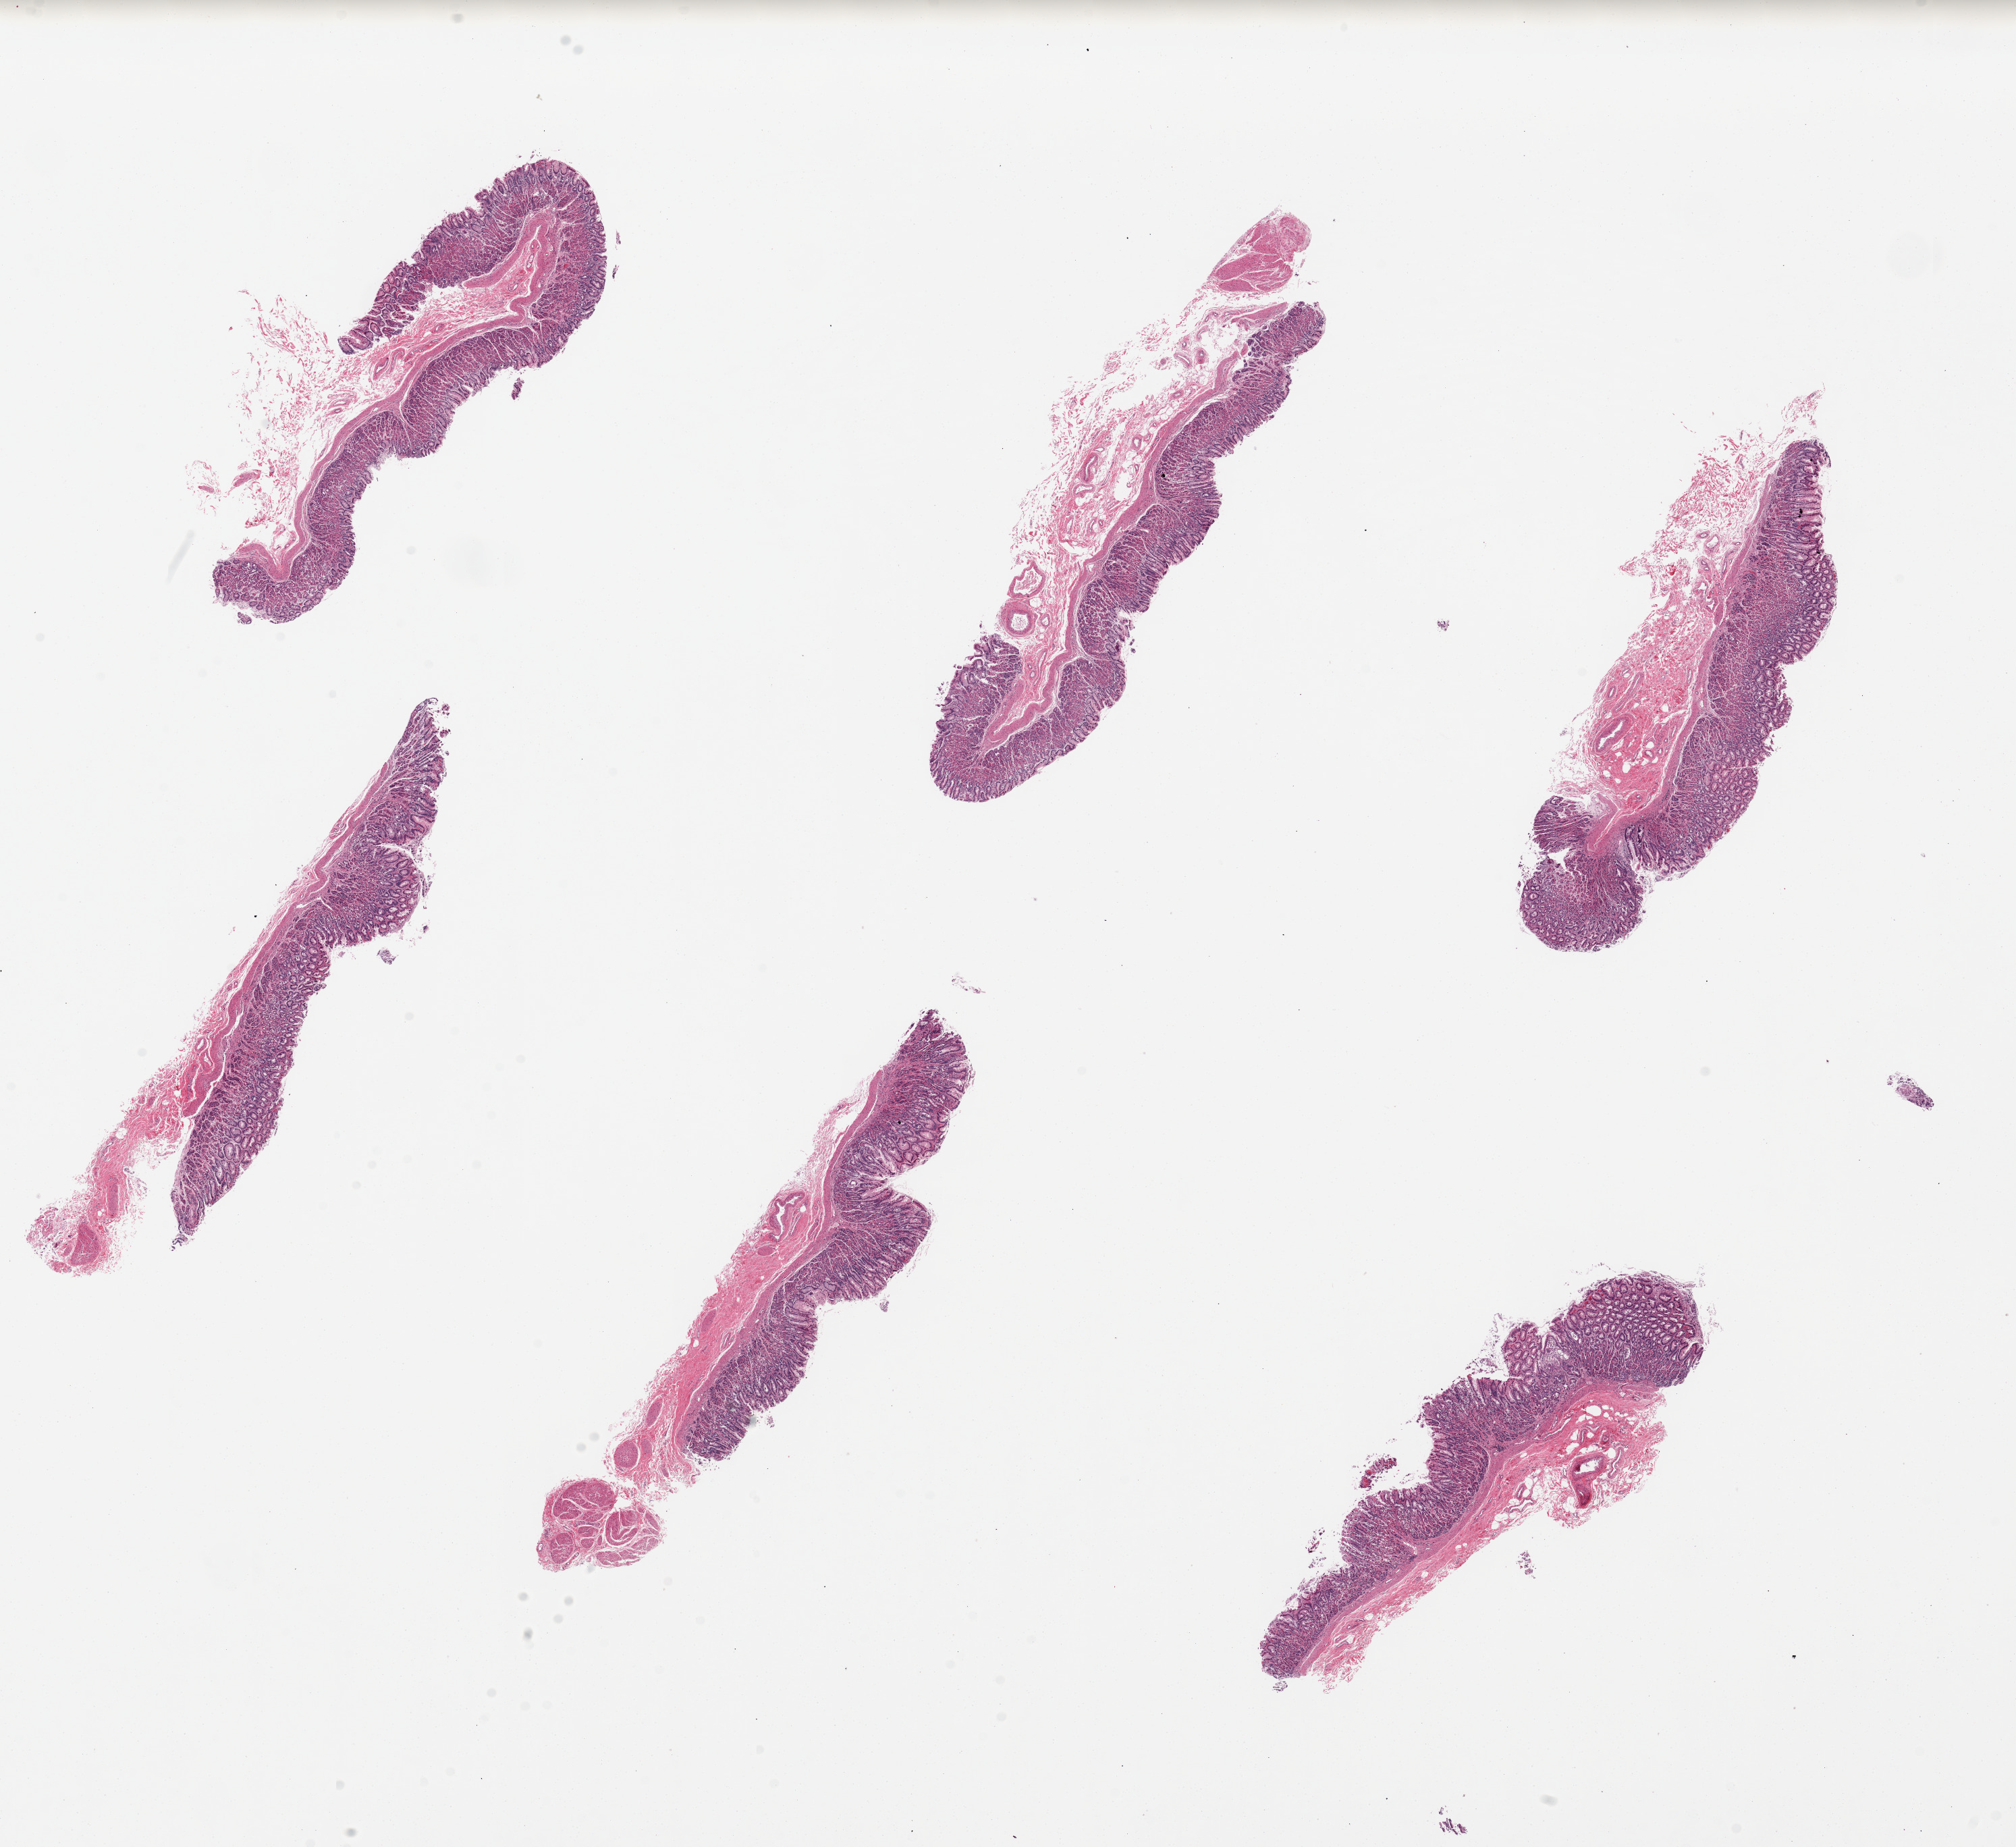
Digitized haematoxylin and eosin-stained section, brightfield — shown as a low-resolution overview of the whole scanned area (about 23.6 x 21.6 mm). PAXgene-fixed, paraffin-embedded tissue. Sampled site (target tissue): stomach. Tissue donor sample. Donor: female.
Review note (as recorded): 6 pieces, up to 8x2mm; All have mucosa and submucosa, no muscularis propria; One piece with small focus of chronic gastritis with intestinal metaplasia; Autolysis varies from 1 to 2.